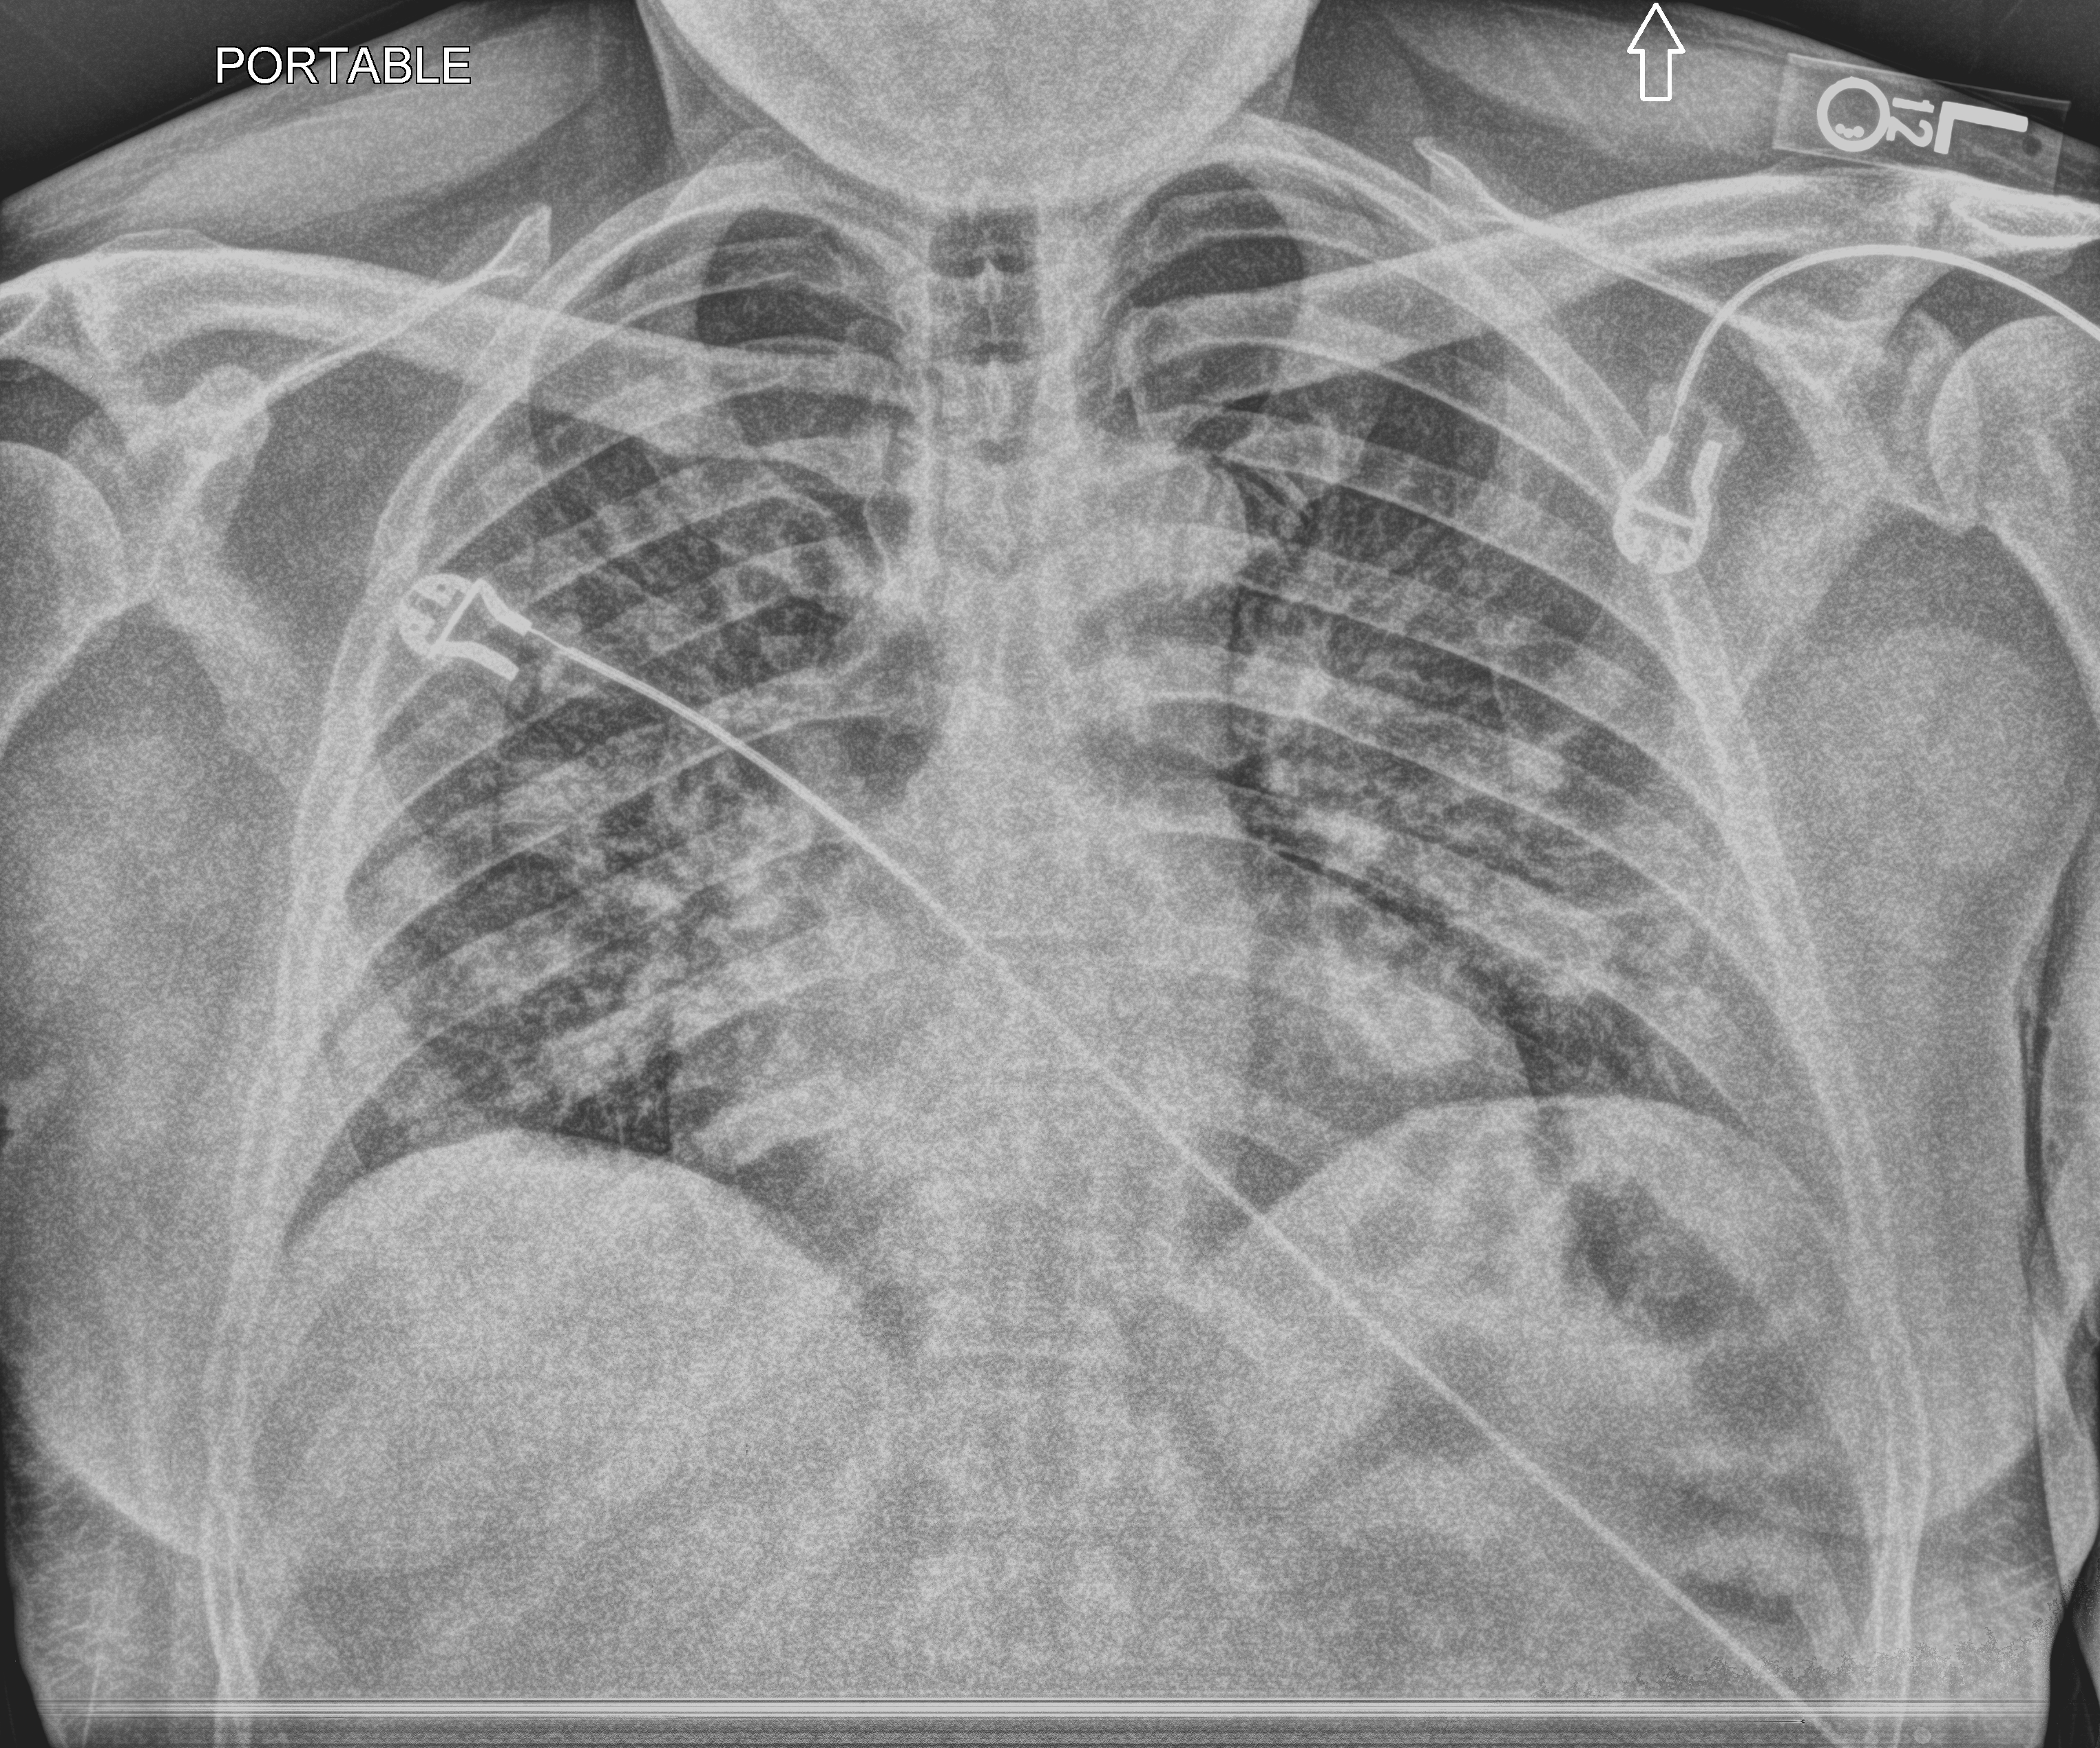
Bedside chest radiograph (computed radiography). Patient hospitalised with COVID-19; male, aged 18–59 years.
From the hospital-stay record, not from the radiograph (when in the stay this image was taken is not recorded): hypertension (admission record): yes; length of hospital stay: 5 days; mechanically ventilated during this hospital stay: no.